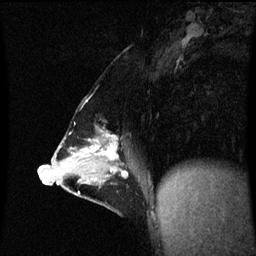
Breast MRI (dynamic contrast-enhanced), one sagittal slice. Position 29 of 60 along the scan axis. Dynamic contrast-enhanced series, image 2 of 3 at this slice position (ordered by acquisition). 1.5 T. TE 4.2 ms, TR 8.9 ms. 256 × 256 image matrix, field of view 200 × 200 mm. Patient: female, 47 years. Case-level facts recorded for this patient, not image findings: setting: breast cancer imaged before/during neoadjuvant chemotherapy; receptor status: HR-positive, HER2-negative.
Structures marked on this image (semi-automatically segmented with operator editing):
- analysis volume of interest (the breast-tissue region the enhancement analysis was run in; not a lesion): bounding box (x1, y1, x2, y2) in pixels: (53, 130, 146, 209)
- tumour enhancement mask (voxels above the 70 % enhancement threshold inside the analysis volume of interest): (63, 132, 129, 177)